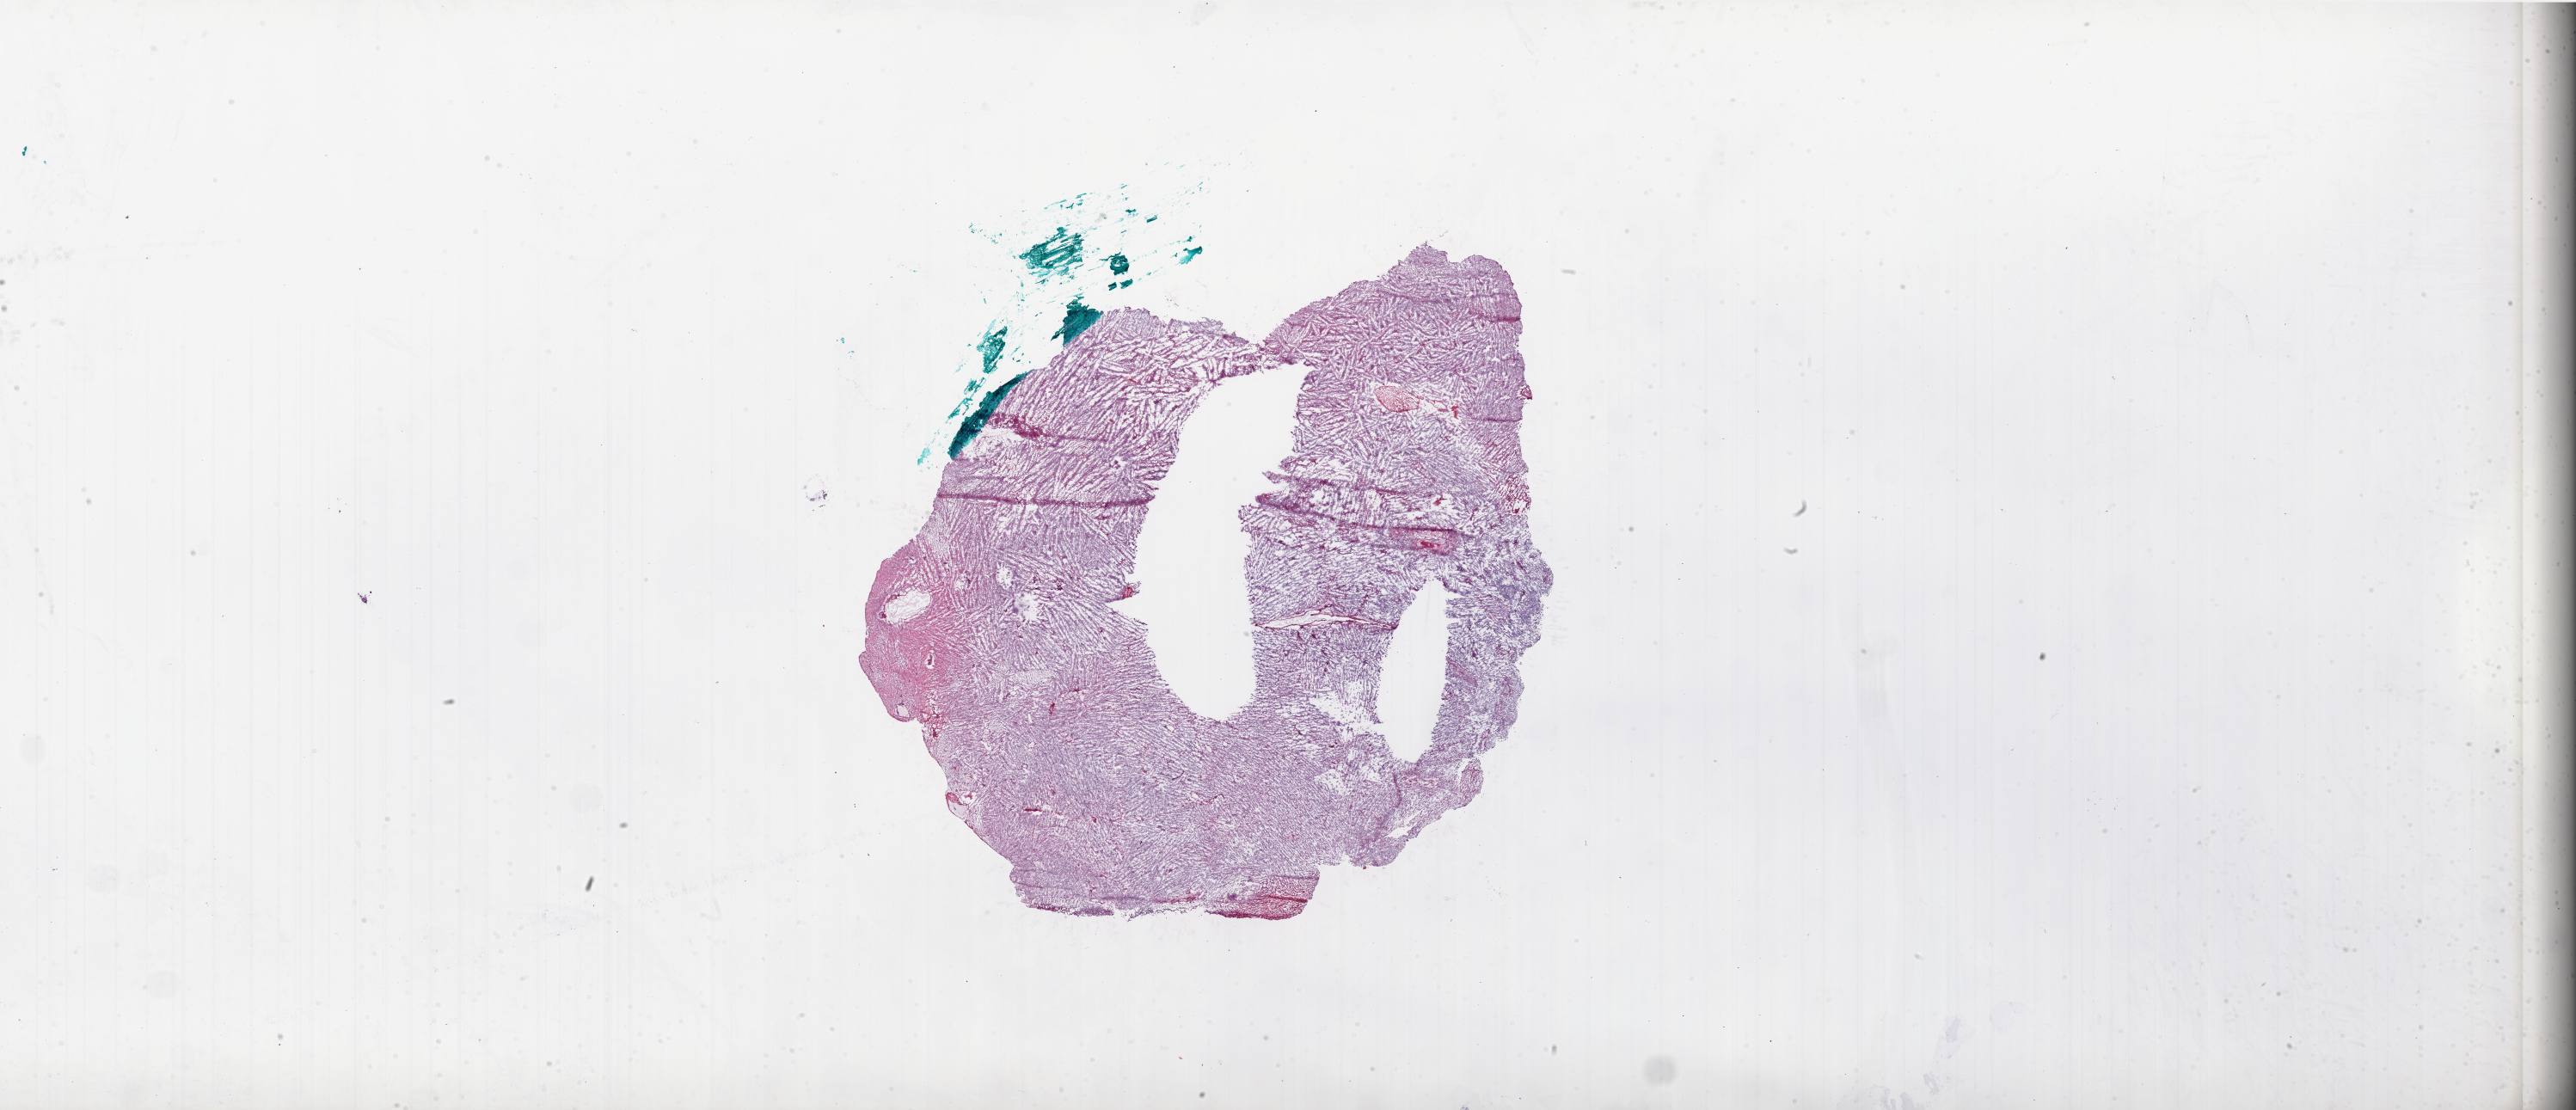
Whole-slide histology image, H&E, whole scanned area (about 48.0 x 20.7 mm, slide scanned at 20x) shown as a low-resolution overview. Frozen section from the bottom of the tissue portion. Brain, primary tumour sample. Male, age 62 years at initial diagnosis.
Histologic diagnosis: Glioblastoma.